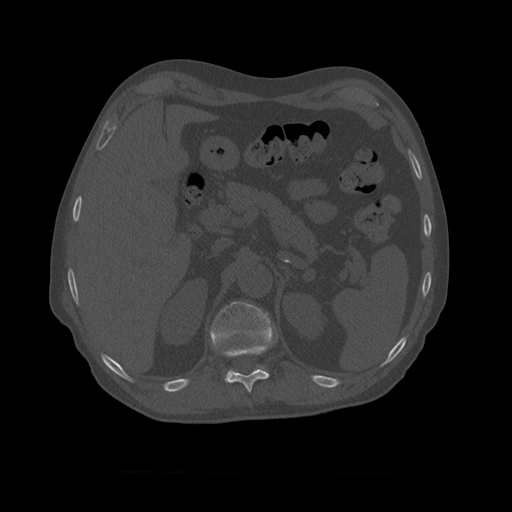
CT including the spine, one axial slice. Slice 394 of 450 in the series (ordered by position). 120 kVp. Bone window (W 1800 / L 400 HU). 1.25 mm slice thickness. 512 × 512 image matrix, field of view 405 × 405 mm. Patient age 75 years. Case-level facts recorded for this patient, not image findings: primary cancer: prostate.
Outlined on this slice (semi-automatically segmented with operator editing):
- T10 vertebra: bounding box <223,344,270,393> (left, top, right, bottom; pixels)
- T11 vertebra: <210,302,278,377>